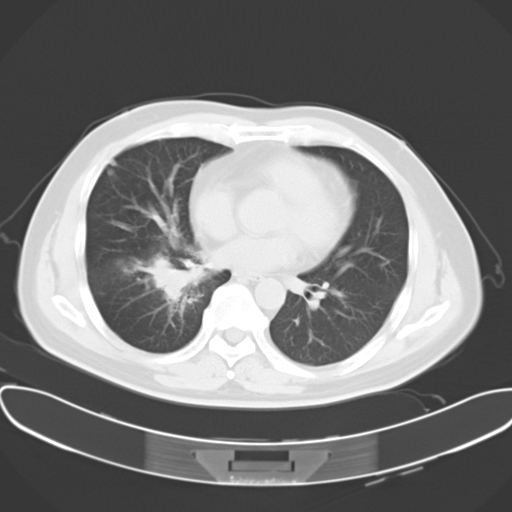
Chest CT, one axial slice; slice 13 of 28 in the series (ordered by position); lung window (W 1500 / L -600 HU); 10 mm slice thickness; 512 × 512 image matrix, field of view 388 × 388 mm. Male patient, age 48 years. Case-level facts recorded for this patient, not image findings: clinical TNM (as recorded): T1a N1 M1c.
Annotated regions visible in this slice (bounding box drawn by a radiologist):
- lung tumour (recorded histology: adenocarcinoma): bounding box [x1, y1, x2, y2] px = [148, 256, 198, 302]